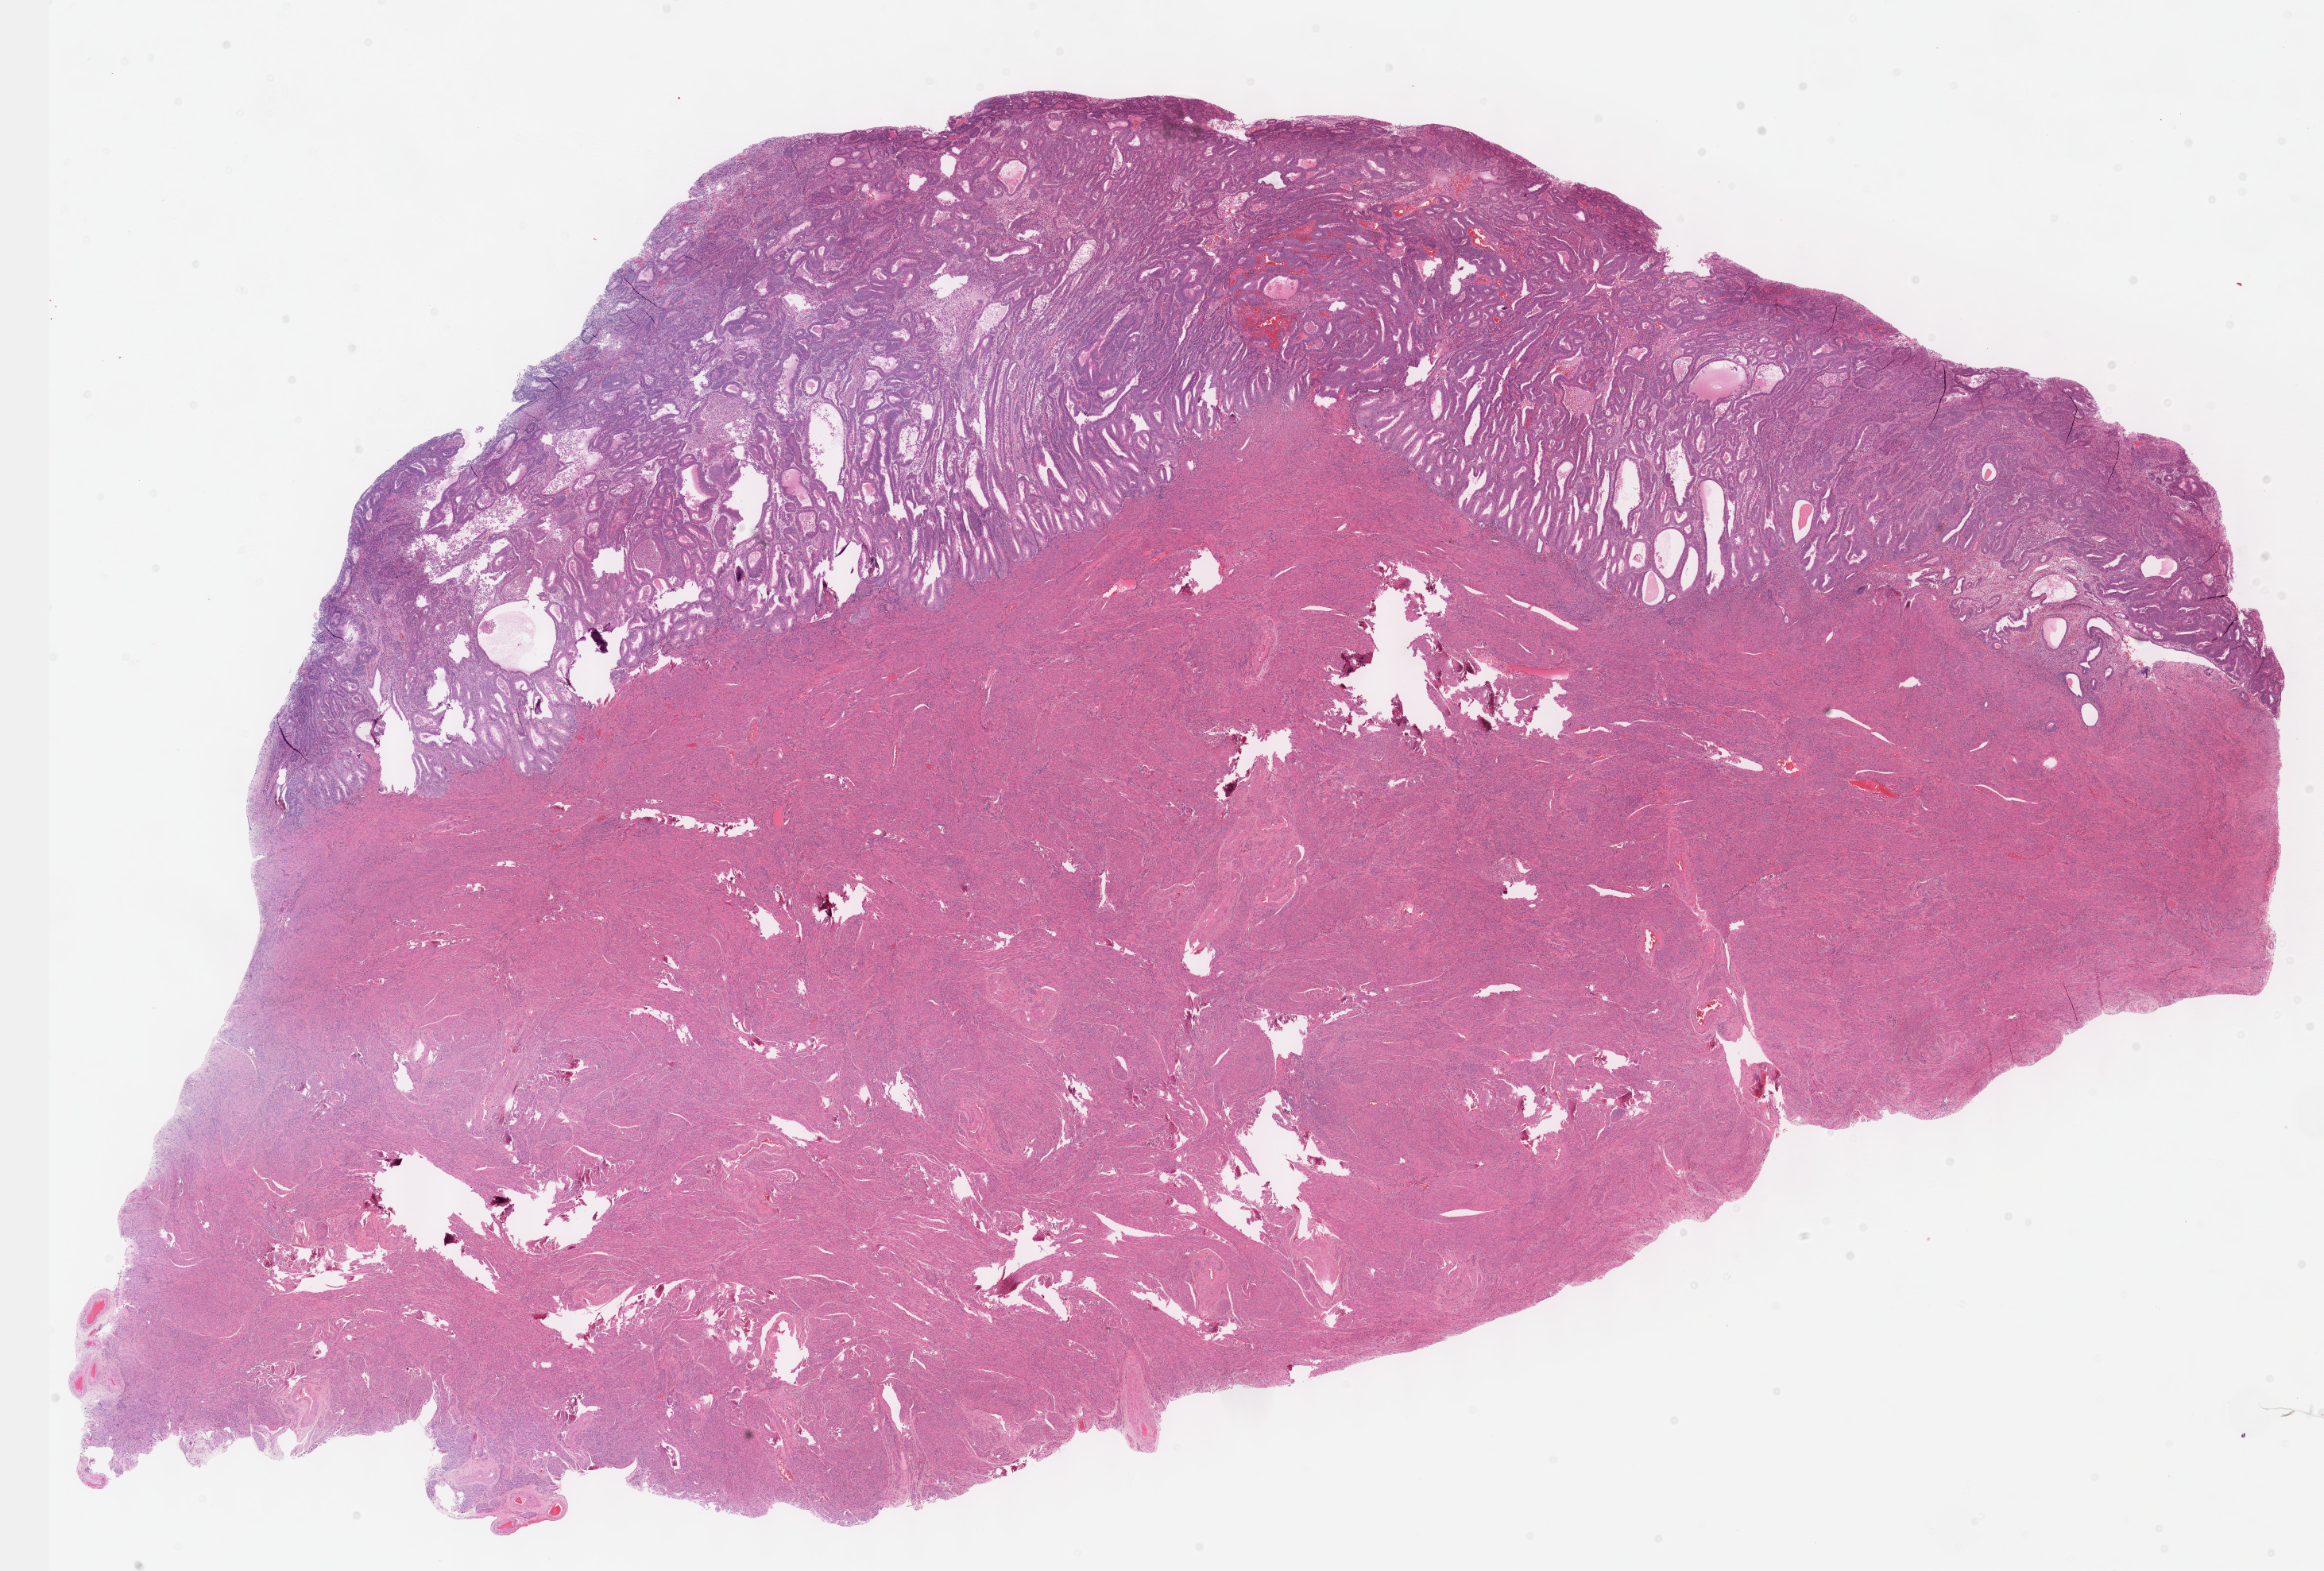
H&E-stained whole-slide image — a low-resolution overview of the entire scanned area, about 23.6 x 16.0 mm (slide scanned at 40x), FFPE section, primary tumour sample from the uterus. Female patient; age at initial diagnosis 70 years. Histologic grade: G2 (moderately differentiated).
• FIGO stage: I
• diagnosis: Endometrioid adenocarcinoma, NOS (endometrium)